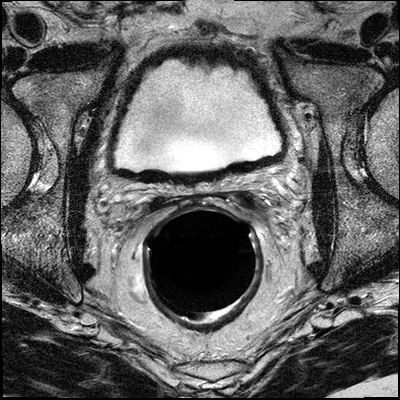
Pelvic MRI after prostatectomy (prostatic bed); 3 images, each a single mid-volume slice chosen by position (not for content). Treatment context recorded for this patient: Surgery.
Image 1: axial T2-weighted image, slice 22 of 42, 3 mm slice thickness.
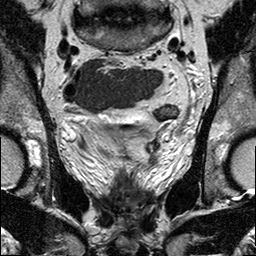
Image 2: coronal T2-weighted image, series "T2W_TSE_COR", slice 17 of 32, 3 mm slice thickness.
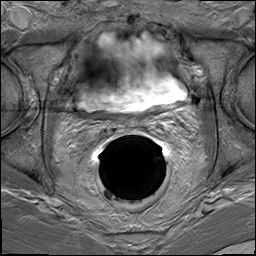
Image 3: DCE (dynamic gadolinium-enhanced) axial slice, series "dyn_THRIVE", slice 22 of 42, dynamic phase 5 of 8, 6 mm slice thickness.
MRI report (verbatim):
Regular findings seen within the surgical bed. Multiple surgical clips within the prostatic bed and around the anastomosis, which obscure (due to expected artifacts) some portions of the surgical bed. Regular appearance of the anastomosis. No definite masses seen within the prostatic bed. No foci of suspicious enhancement in and around the prostatic bed. Unremarkable urinary bladder. No remnant seminal vesicles present. No suspiciously enlarged obturator and iliac lymph nodes. Several small lymph nodes all sub 5 mm seen along the iliac vessels, The there is a perirectal round lymph node on the left at 9 o'clock, which measures 4 mm. The visualized osseous structures without evidence of malignant involvement. Incidental note is made of Sigma diverticulosis. IMPRESSION: 1) No manifest residual tumor; no discrete mass. 2) No remnant seminal vesicls. 3) Expected appearance of the prostatic bed and anastomosis (after surgery 6 weeks ago). 4) No enlarged obturator or iliac lymph nodes. Small 4 mm left perirectal lymph node, of unknown significance. 5) Incidental note is made of Sigma diverticulosis. Radiation therapy is considered. Pre-planning MRI; evaluation for local residual tumor. FINDINGS: Regular findings seen within the surgical bed. Multiple surgical clips within the prostatic bed and around the anastomosis, which obscure (due to expected artifacts) some portions of the surgical bed. Regular appearance of the anastomosis. No definite masses seen within the prostatic bed. No foci of suspicious enhancement in and around the prostatic bed. Unremarkable urinary bladder. No remnant seminal vesicles present. No suspiciously enlarged obturator and iliac lymph nodes. Several small lymph nodes all sub 5 mm seen along the iliac vessels, The there is a perirectal round lymph node on the left at 9 o'clock, which measures 4 mm. (series 401 slice location 78) The visualized osseous structures without evidence of malignant involvement. IMPRESSION: 1) No manifest residual tumor; no discrete mass. 2) No remnant seminal vesicals. 3) Expected appearance of the prostatic bed and anastomosis (after surgery 6 weeks ago). 4) No enlarged obturator or iliac lymph nodes. Small 4 mm left perirectal lymph node, of unknown significance.

Prostatectomy specimen pathology (as recorded; the prostatectomy preceded this MRI, which images the post-surgical bed):
A: PROSTATE AND RIGHT SEMINAL VESICLE B: RIGHT INTERNAL ILIAC AND OBTURATOR NODES C: LEFT INTERNAL ILIAC AND OBTURATOR NODES D: LEFT SEMINAL VESICLE E: BASE OF PROSTATE A. PROSTATE AND RIGHT SEMINAL VESICLE: Procedure Radical prostatectomy Prostate Size: Weight: 42.1grams Size: 4.2 x 4.1x 4.1 cm Lymph Node Sampling: Pelvic lymph node dissection Histologic Type: Adenocarcinoma (acinar, not otherwise specified) Histologic Grade: Primary Pattern: Grade 4 Secondary Pattern Grade 3 Total Gleason Score: 7 Tumor Quantitation: Proportion (percentage) of prostate involved by tumor: 80% Extraprostatic Extension: Present, Focal. Seminal Vesicle Invasion: Present. Margins Margin(s) involved by invasive carcinoma: Bladder neck Treatment Effect of Carcinoma Not identified Lymph-Vascular Invasion Not identified Perineural Invasion Present Pathologic Staging (pTNM) Primary Tumor (pT) pT3: Extraprostatic extension pT3b: Seminal vesicle invasion Regional Lymph Nodes (pN) pN0: No regional lymph node metastasis Specify: Number involved: 0 Distant Metastasis (pM) pMx: Not applicable Additional Pathologic Findings: High-grade prostatic intraepithelial neoplasia (PIN), Chronic Inflammation. Gross Description A. "Prostate and Right Seminal Vesicle", B. "Right Internal Ilial and Obturator Nodes", C. "Left External Iliac and Obturator Nodes", D. "Left Seminal Vesicle" and E. "Base of Prostate". Specimen A consists of a prostatectomy specimen weighing 42.1 gms. The prostate measures 4.2 x 4.1 x 4.1 cm. The right seminal vesicle measures 3.9 x 1.3 x 1.0 cm. The right vas deferens measures 5.5 in length by 0.5 cm in diameter. The left vas deferens measures 5.6 cm in length by 0.5 cm in diameter. The right aspect of the specimen is inked black and the left aspect is inked blue. The specimen is submitted in toto in cassettes as follows: A1 left vas deferens, A2 right seminal vesicle, A3 bladder margin, A4 apical margin, A5 thru A10 left superior lobe from apical to bladder margin, A11 thru A18 left inferior lobe from apical to bladder margin, A19 thru A25 right inferior lobe from apical to bladder margin, and A26 thru A31 right superior lobe from apical to bladder margin and A32- right vas deferens. Specimen B consists of a segment of fibroadipose tissue measuring 2.5 x 2.5 x 2.5 cm. Two potential lymph nodes are identified measuring 1.5 x 1.4 x 1.3 cm and 1.4 x 1.2 x 1.2 cm. The specimen is submitted in toto in cassettes as follows: B1 one lymph node bisected, B2 one lymph node bisected, and B3 and B4 remaining fat. Specimen C consists of a fragment of fibroadipose tissue measuring 2.0 x 1.5 x 1.5 cm. No potential lymph nodes are identified. The specimen is submitted in toto in two cassettes labeled C1 and C2. Specimen D consists of a seminal vesicle measuring 3.0 x 1.5 x 1.0 cm. Specimen E consists of a fragment of soft tan tissue measuring 1.0 x 0.9 x 0.9 cm. The specimen is submitted in toto in a single cassette labeled E. Specimen: A: PROSTATE AND RIGHT SEMINAL VESICLE B: RIGHT INTERNAL ILIAC AND OBTURATOR NODES C: LEFT INTERNAL ILIAC AND OBTURATOR NODES D: LEFT SEMINAL VESICLE E: BASE OF PROSTATE A. PROSTATE AND RIGHT SEMINAL VESICLE: Procedure: Radical prostatectomy Prostate Size: Weight: 42.1grams Size: 4.2 x 4.1x 4.1 cm Histologic Type: Adenocarcinoma (acinar) Histologic Grade: Primary Pattern: Grade 4 Secondary Pattern Grade 3 Total Gleason Score: 7 Tumor Quantitation: Proportion (percentage) of prostate involved by tumor: 80% Extraprostatic Extension: Present, Focal (Left inferior lobe). Seminal Vesicle Invasion:Present (Left seminal vesicle) Margin(s) involved by invasive carcinoma: Bladder neck. Perineural Invasion Present Pathologic Staging (pTNM) Primary Tumor (pT) pT3: Extraprostatic extension pT3b: Seminal vesicle invasion (left seminal vesicle). Regional Lymph Nodes (pN) pN0:No regional lymph node metastasis. Number examined: 8 Number involved: 0 E. BASE OF PROSTATE: PROSTATIC TISSUE WITH ADENOCARCINOMA, GLEASON SCORE: 4+3=7/10.